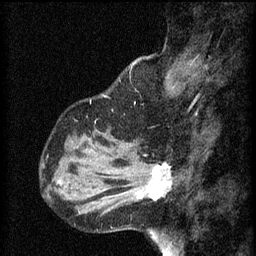
Breast MRI (dynamic contrast-enhanced), one sagittal slice; slice 16 of 60 in the series (ordered by position); 3 images stored at this slice position (order not interpretable as contrast timing); 1.5 T; TE 4.2 ms, TR 8.2 ms; 2 mm slice thickness; 256 × 256 image matrix, field of view 180 × 180 mm. Female patient, age 37 years.
Outlined on this slice (semi-automatic segmentation, software-assisted and operator-edited):
- analysis volume of interest (the breast-tissue region the enhancement analysis was run in; not a lesion): bounding box <126,156,175,205> (left, top, right, bottom; pixels)
- tumour enhancement mask (voxels above the 70 % enhancement threshold inside the analysis volume of interest): <137,164,172,201>